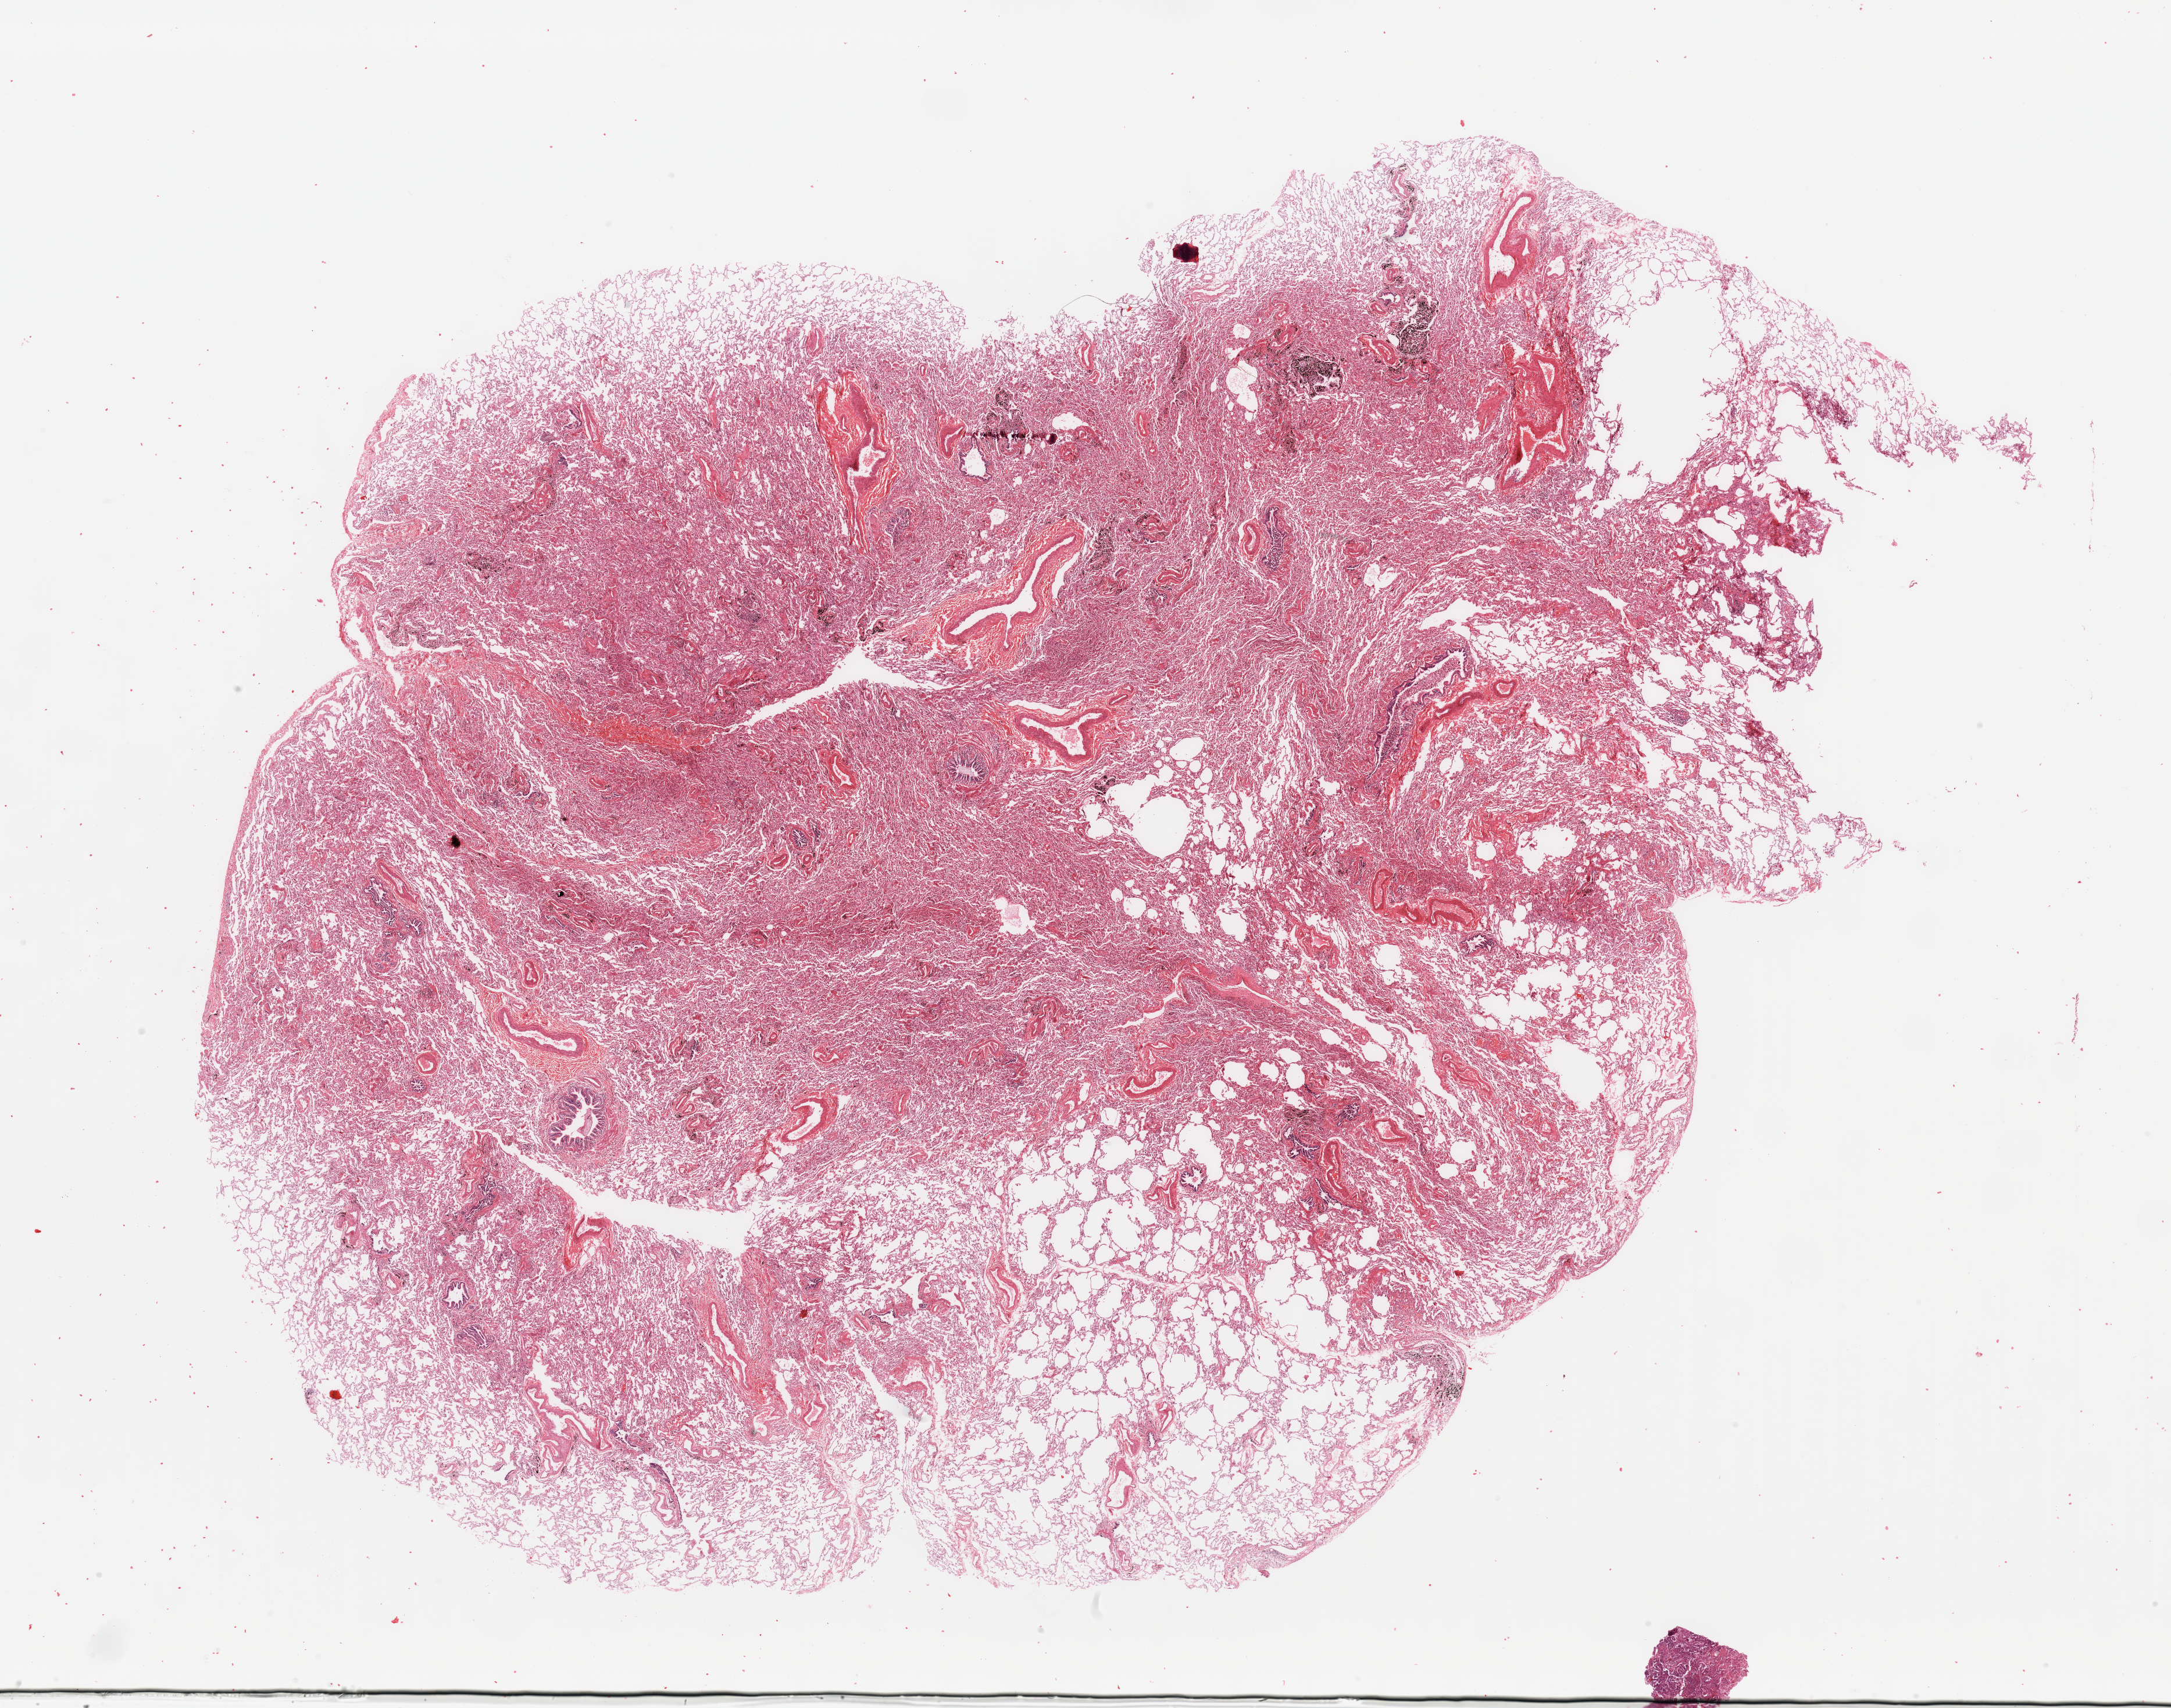
Whole-slide histology image, H&E-stained, shown as a low-resolution overview of the whole scanned area (about 29.5 x 23.2 mm, acquisition: 20x scan). Normal (non-tumour) tissue sample, sampled site: lung. Patient: male, age 61 years.
* this section: normal (non-tumour) tissue from the same patient
* patient diagnosis: Adenocarcinoma, NOS